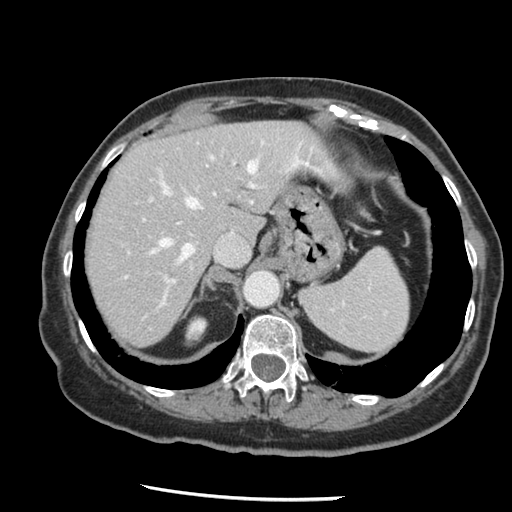
Contrast-enhanced abdominal CT, one axial slice; position 102 of 148 along the scan axis; intravenous contrast given; soft-tissue window (W 400 / L 40 HU); 2.5 mm slice thickness; 512 × 512 image matrix, field of view 330 × 330 mm. Female patient, age 85 years. From the clinical record (not read from this slice): diagnosis: colorectal cancer liver metastases, imaged before liver resection; multiple liver metastases: no.
Outlined on this slice (expert manual segmentation):
- hepatic veins: bounding box <148,139,294,262> (left, top, right, bottom; pixels)
- liver: <85,121,328,347>
- planned liver remnant (the part of the liver to remain after resection): <85,121,328,347>
- portal vein (with intrahepatic branches): <143,156,256,308>